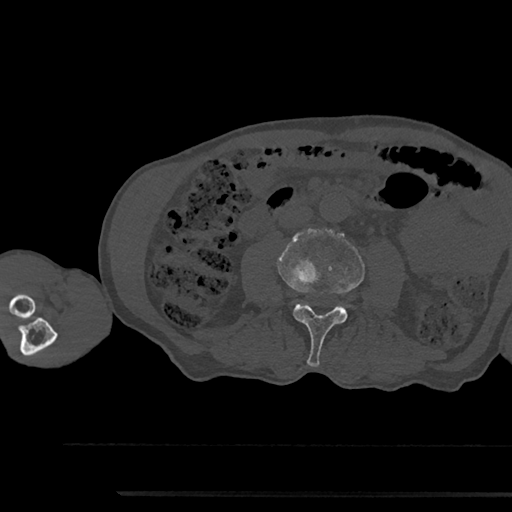
CT including the spine, one axial slice. Position 473 of 797 along the scan axis. Bone window (W 1800 / L 400 HU). 0.5 mm slice thickness. 512 × 512 image matrix, field of view 367 × 367 mm. Patient: male, 79 years. Case-level facts recorded for this patient, not image findings: primary cancer: prostate.
Annotated regions visible in this slice (semi-automatically segmented with operator editing):
- L3 vertebra: bounding box <278,229,365,367> (left, top, right, bottom; pixels)